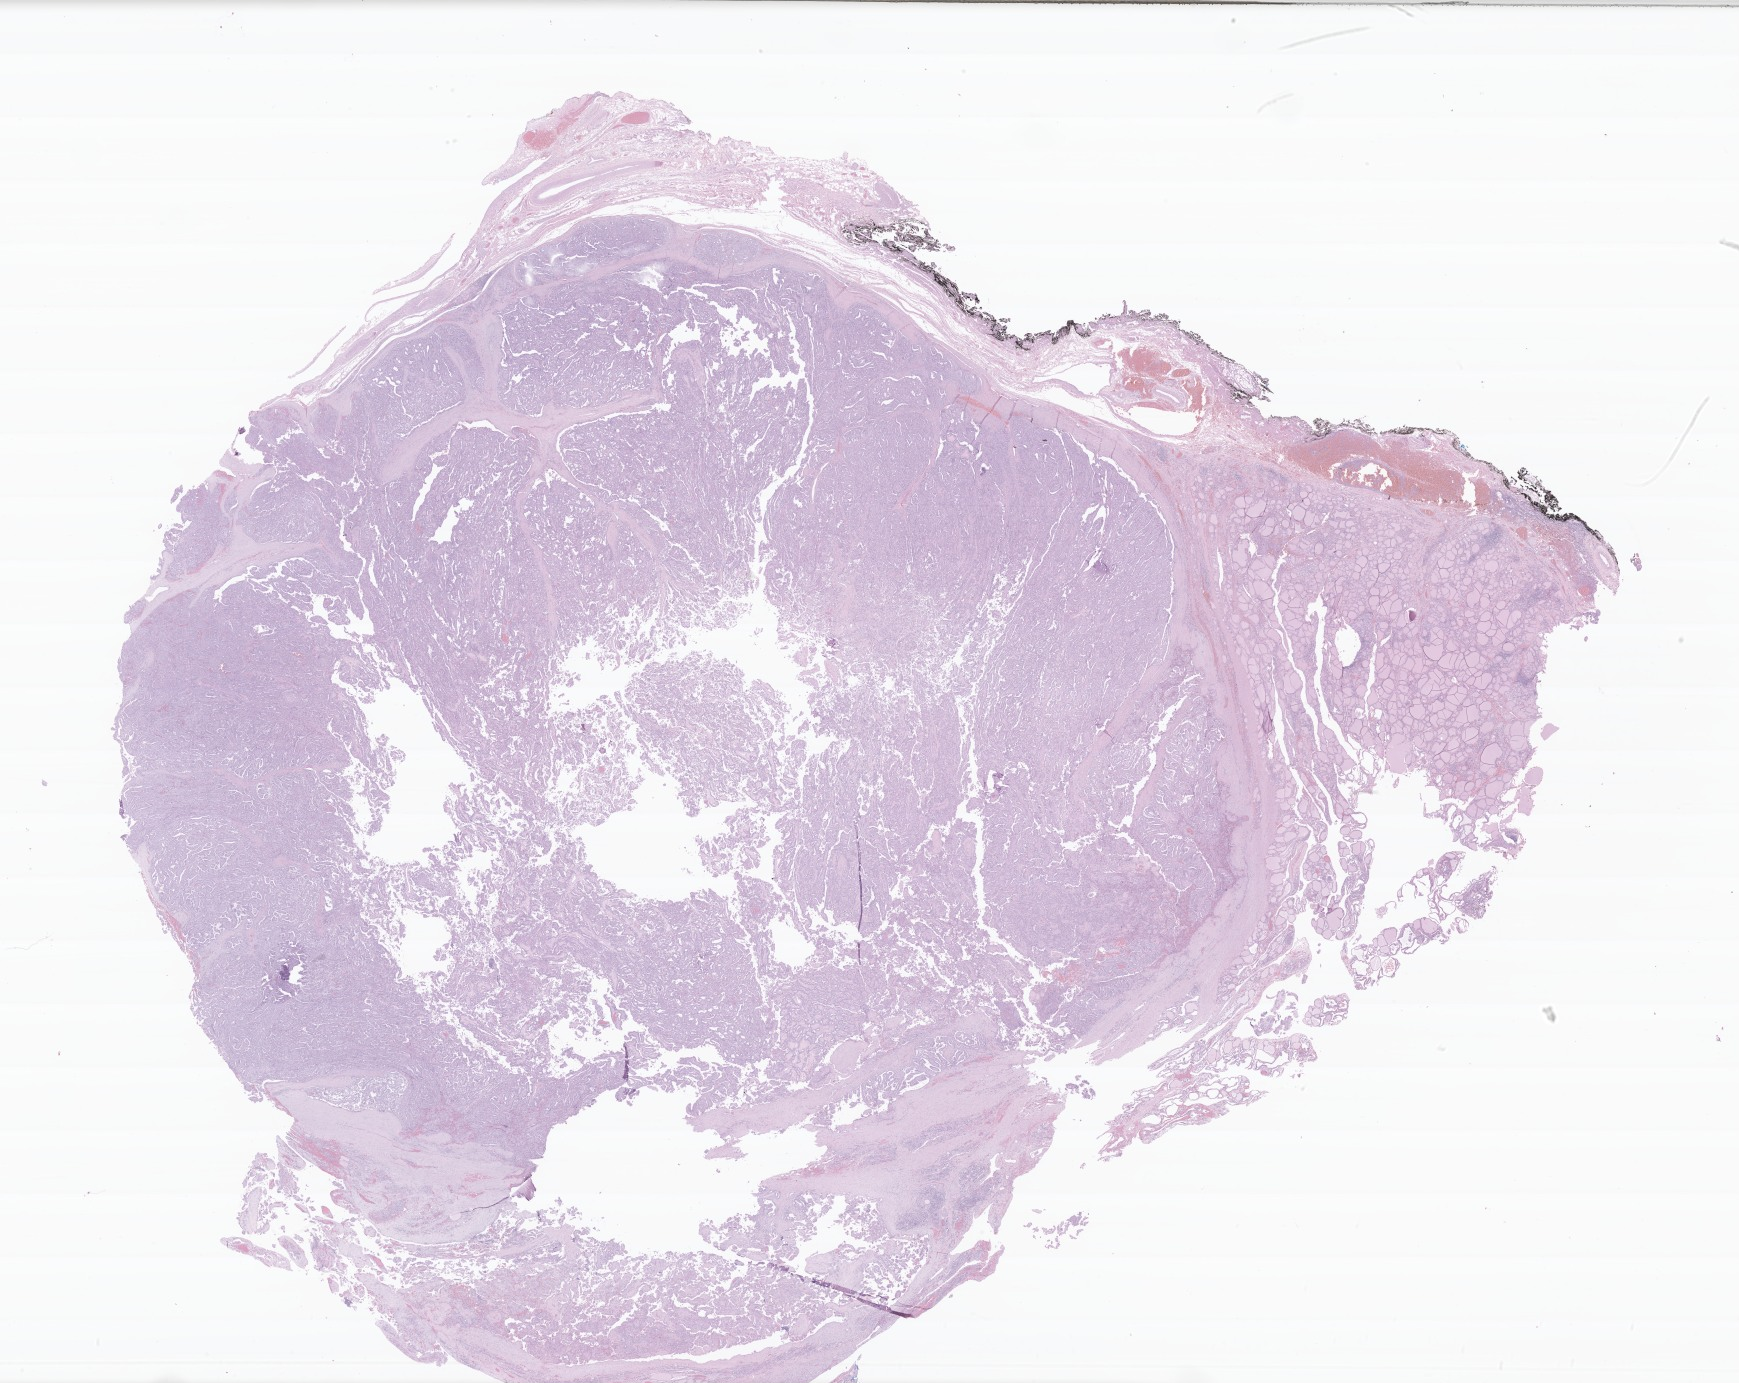
Whole-slide image, haematoxylin and eosin stain of tumor tissue from the thyroid — shown as a low-resolution overview of the whole scanned area (about 29.3 x 23.3 mm), formalin-fixed paraffin-embedded section. Patient female; age 217 months (18 years 1 month).
Diagnosis: Papillary carcinoma, NOS.